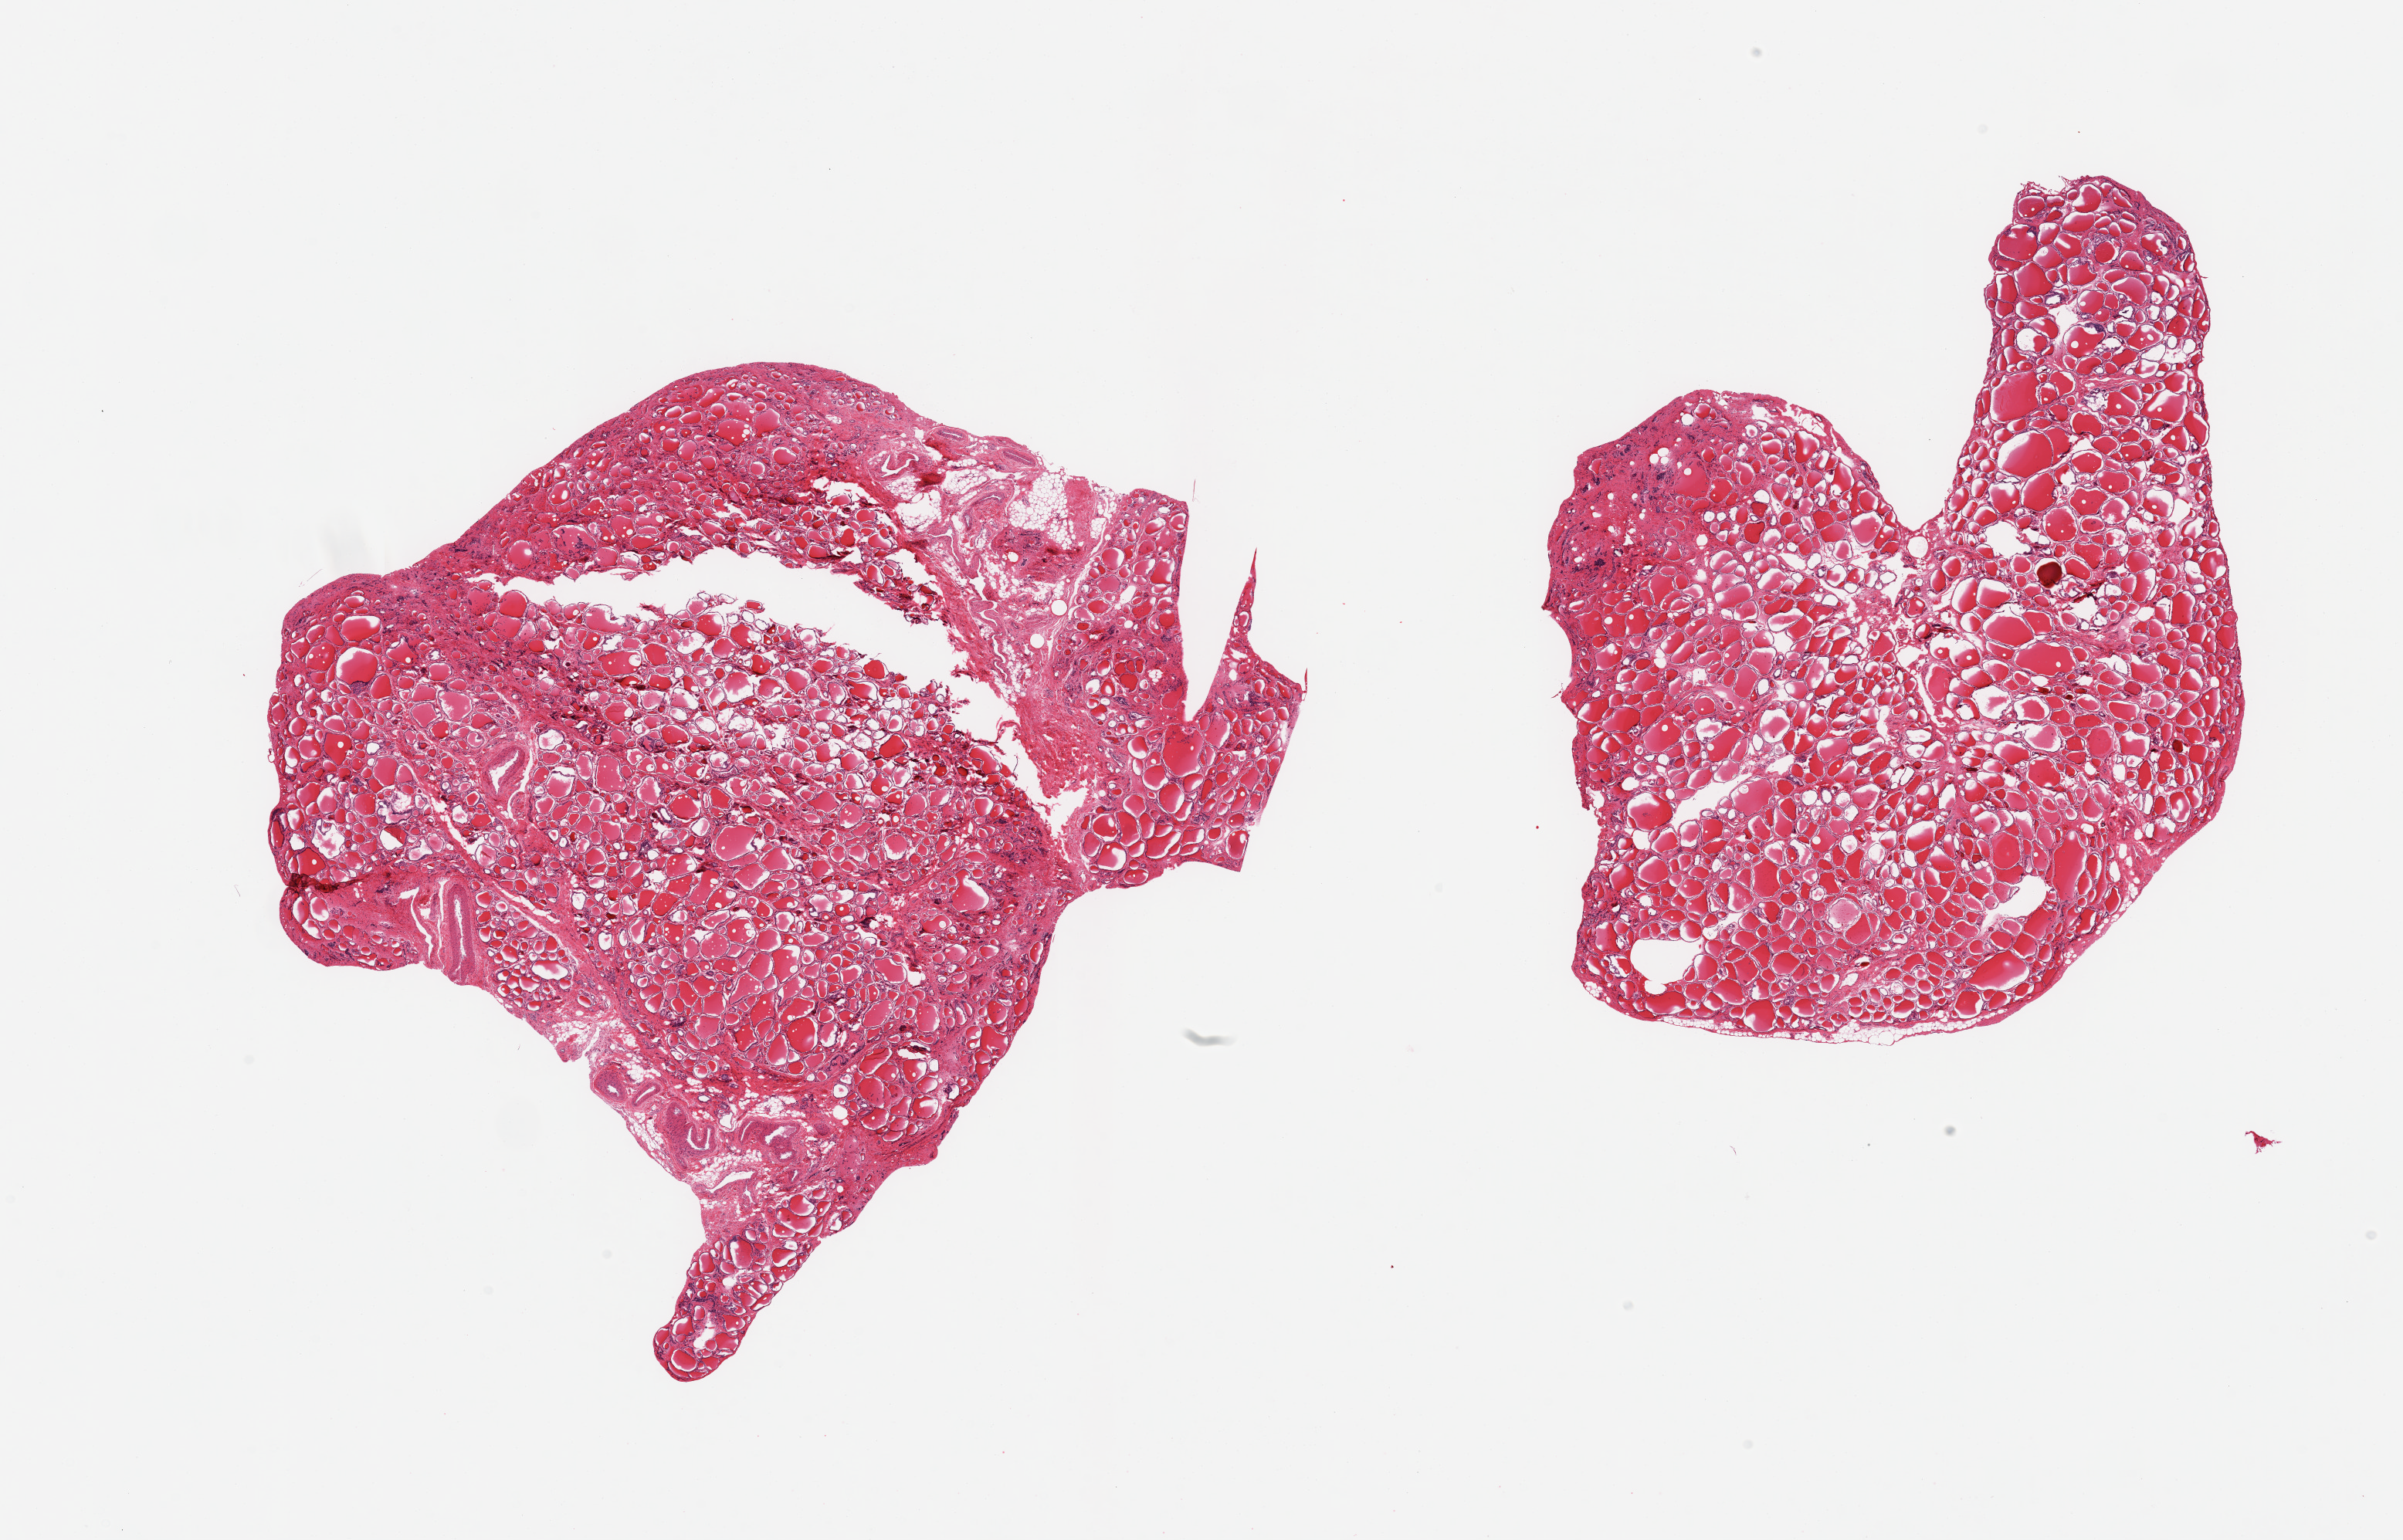
Whole-slide image, H&E stain — whole scanned area (about 24.6 x 15.8 mm) shown as a low-resolution overview; PAXgene-fixed paraffin-embedded (PFPE) section; section of thyroid (target tissue); donor tissue sample. Donor: male.
Pathologist's review note for this sample: 2 pieces; mild interstitial fibrosis, ~10% is fat/fibrous/vessels.